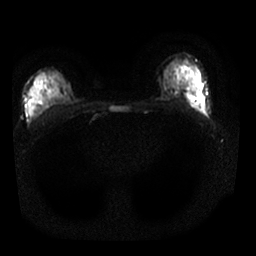
Breast MRI, one axial slice. Slice 15 of 25 in the series (ordered by position). Diffusion-weighted series; image 2 of 4 stored at this slice position (different b-values; order by instance number). 1.5 T. 4 mm slice thickness. 256 × 256 image matrix, field of view 320 × 320 mm. Female patient.
Annotated regions visible in this slice (outlined manually by an expert reader):
- tumour on diffusion-weighted imaging: box from (x=189, y=96) to (x=200, y=108) px